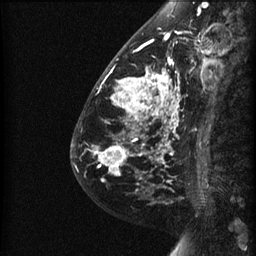
Breast MRI (dynamic contrast-enhanced), one sagittal slice; slice 19 of 60 in the series (ordered by position); dynamic contrast-enhanced series, image 2 of 3 at this slice position (ordered by acquisition); 1.5 T; TE 4.2 ms, TR 22.7 ms; 1.5 mm slice thickness; 256 × 256 image matrix, field of view 180 × 180 mm. Patient: female, 48 years. Case-level facts recorded for this patient, not image findings: setting: breast cancer imaged before/during neoadjuvant chemotherapy; receptor status: triple-negative.
Outlined on this slice (semi-automatic segmentation, software-assisted and operator-edited):
- analysis volume of interest (the breast-tissue region the enhancement analysis was run in; not a lesion): bounding box <89,27,191,180> (left, top, right, bottom; pixels)
- tumour enhancement mask (voxels above the 90 % enhancement threshold inside the analysis volume of interest): <98,28,188,180>